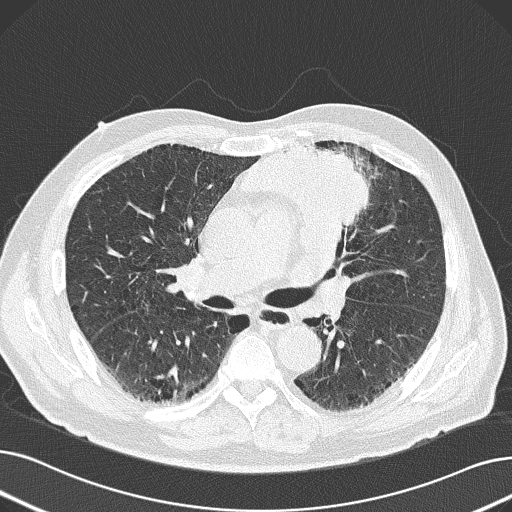
Chest CT (low-dose screening protocol), one axial image; first (baseline) screen; lung window (W 1500 / L -600 HU); 2 mm slice thickness. Male participant, aged 69 years at enrolment. Former smoker at enrolment.
Expert reader's lesion annotation, bounding box (x1, y1, x2, y2) in pixels: (237, 131, 385, 249). The exam's reader record, not a measurement of the box and not confirmed to be the same lesion: non-calcified nodule or mass ≥4 mm, left upper lobe, 6 × 10 mm, spiculated (stellate) margins, soft tissue attenuation. Official screen result: positive, change unspecified: nodule(s) >= 4 mm or enlarging nodule(s), mass(es), or other non-specific abnormalities suspicious for lung cancer. Participant outcome: lung cancer diagnosed 20 days after this screen — non-small cell carcinoma, left upper lobe, poorly differentiated (G3), stage IB (AJCC 6th edition), 100 mm at pathology.